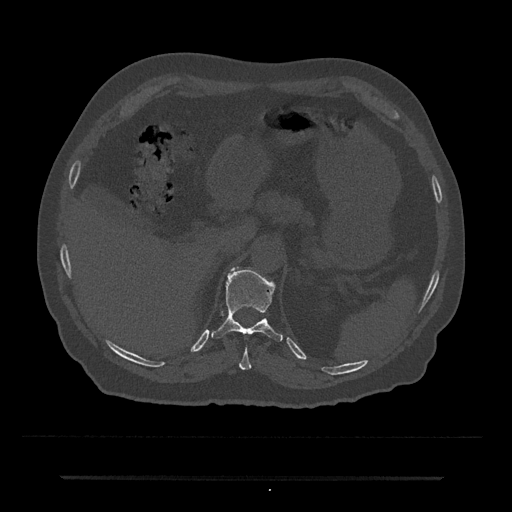
CT including the spine, one axial slice. Position 184 of 797 along the scan axis. Reconstruction kernel Br40s/3. Bone window (W 1800 / L 400 HU). 512 × 512 image matrix, field of view 437 × 437 mm. Patient: male, 69 years. From the clinical record (not read from this slice): primary cancer: prostate.
Structures marked on this image (semi-automatically segmented with operator editing):
- T10 vertebra: bounding box [x1, y1, x2, y2] px = [239, 347, 252, 370]
- T11 vertebra: [211, 267, 283, 342]